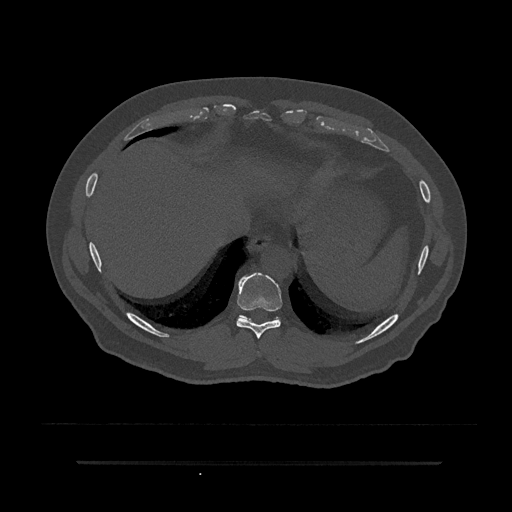
CT including the spine, one axial slice; position 367 of 797 along the scan axis; reconstruction kernel Br40s/3; 120 kVp; bone window (W 1800 / L 400 HU); 0.5 mm slice thickness; 512 × 512 image matrix, field of view 464 × 464 mm. Patient: male, 59 years. From the clinical record (not read from this slice): primary cancer: bile ducts; vertebrae with lytic lesions (as recorded): T10.
Structures marked on this image (semi-automatic segmentation, software-assisted and operator-edited):
- T10 vertebra: bounding box [x1, y1, x2, y2] px = [274, 318, 278, 320]
- T9 vertebra: [236, 273, 282, 339]